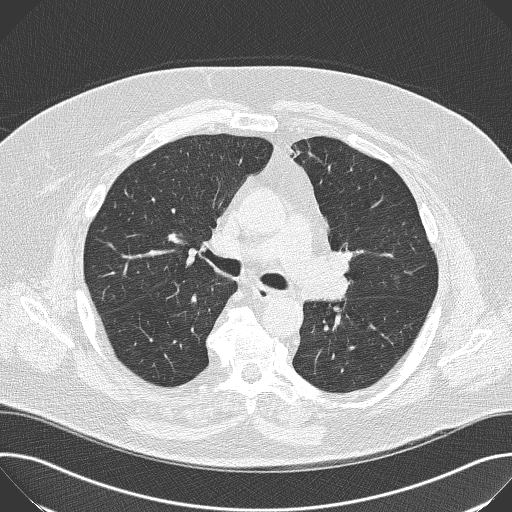
Low-dose screening chest CT, axial slice; baseline screening round; lung window (W 1500 / L -600 HU); 2 mm slice thickness; 512 × 512 image matrix, field of view 380 × 380 mm. Male participant, aged 68 years at enrolment. Former smoker at enrolment.
Expert-annotated lung lesion, bounding box <318,233,370,283> (left, top, right, bottom; pixels). The screening reader recorded 2 non-calcified nodules or masses ≥4 mm on this exam (left lower lobe, right lower lobe); which of them this box marks is not recorded. Official screen result: positive, change unspecified: nodule(s) >= 4 mm or enlarging nodule(s), mass(es), or other non-specific abnormalities suspicious for lung cancer.